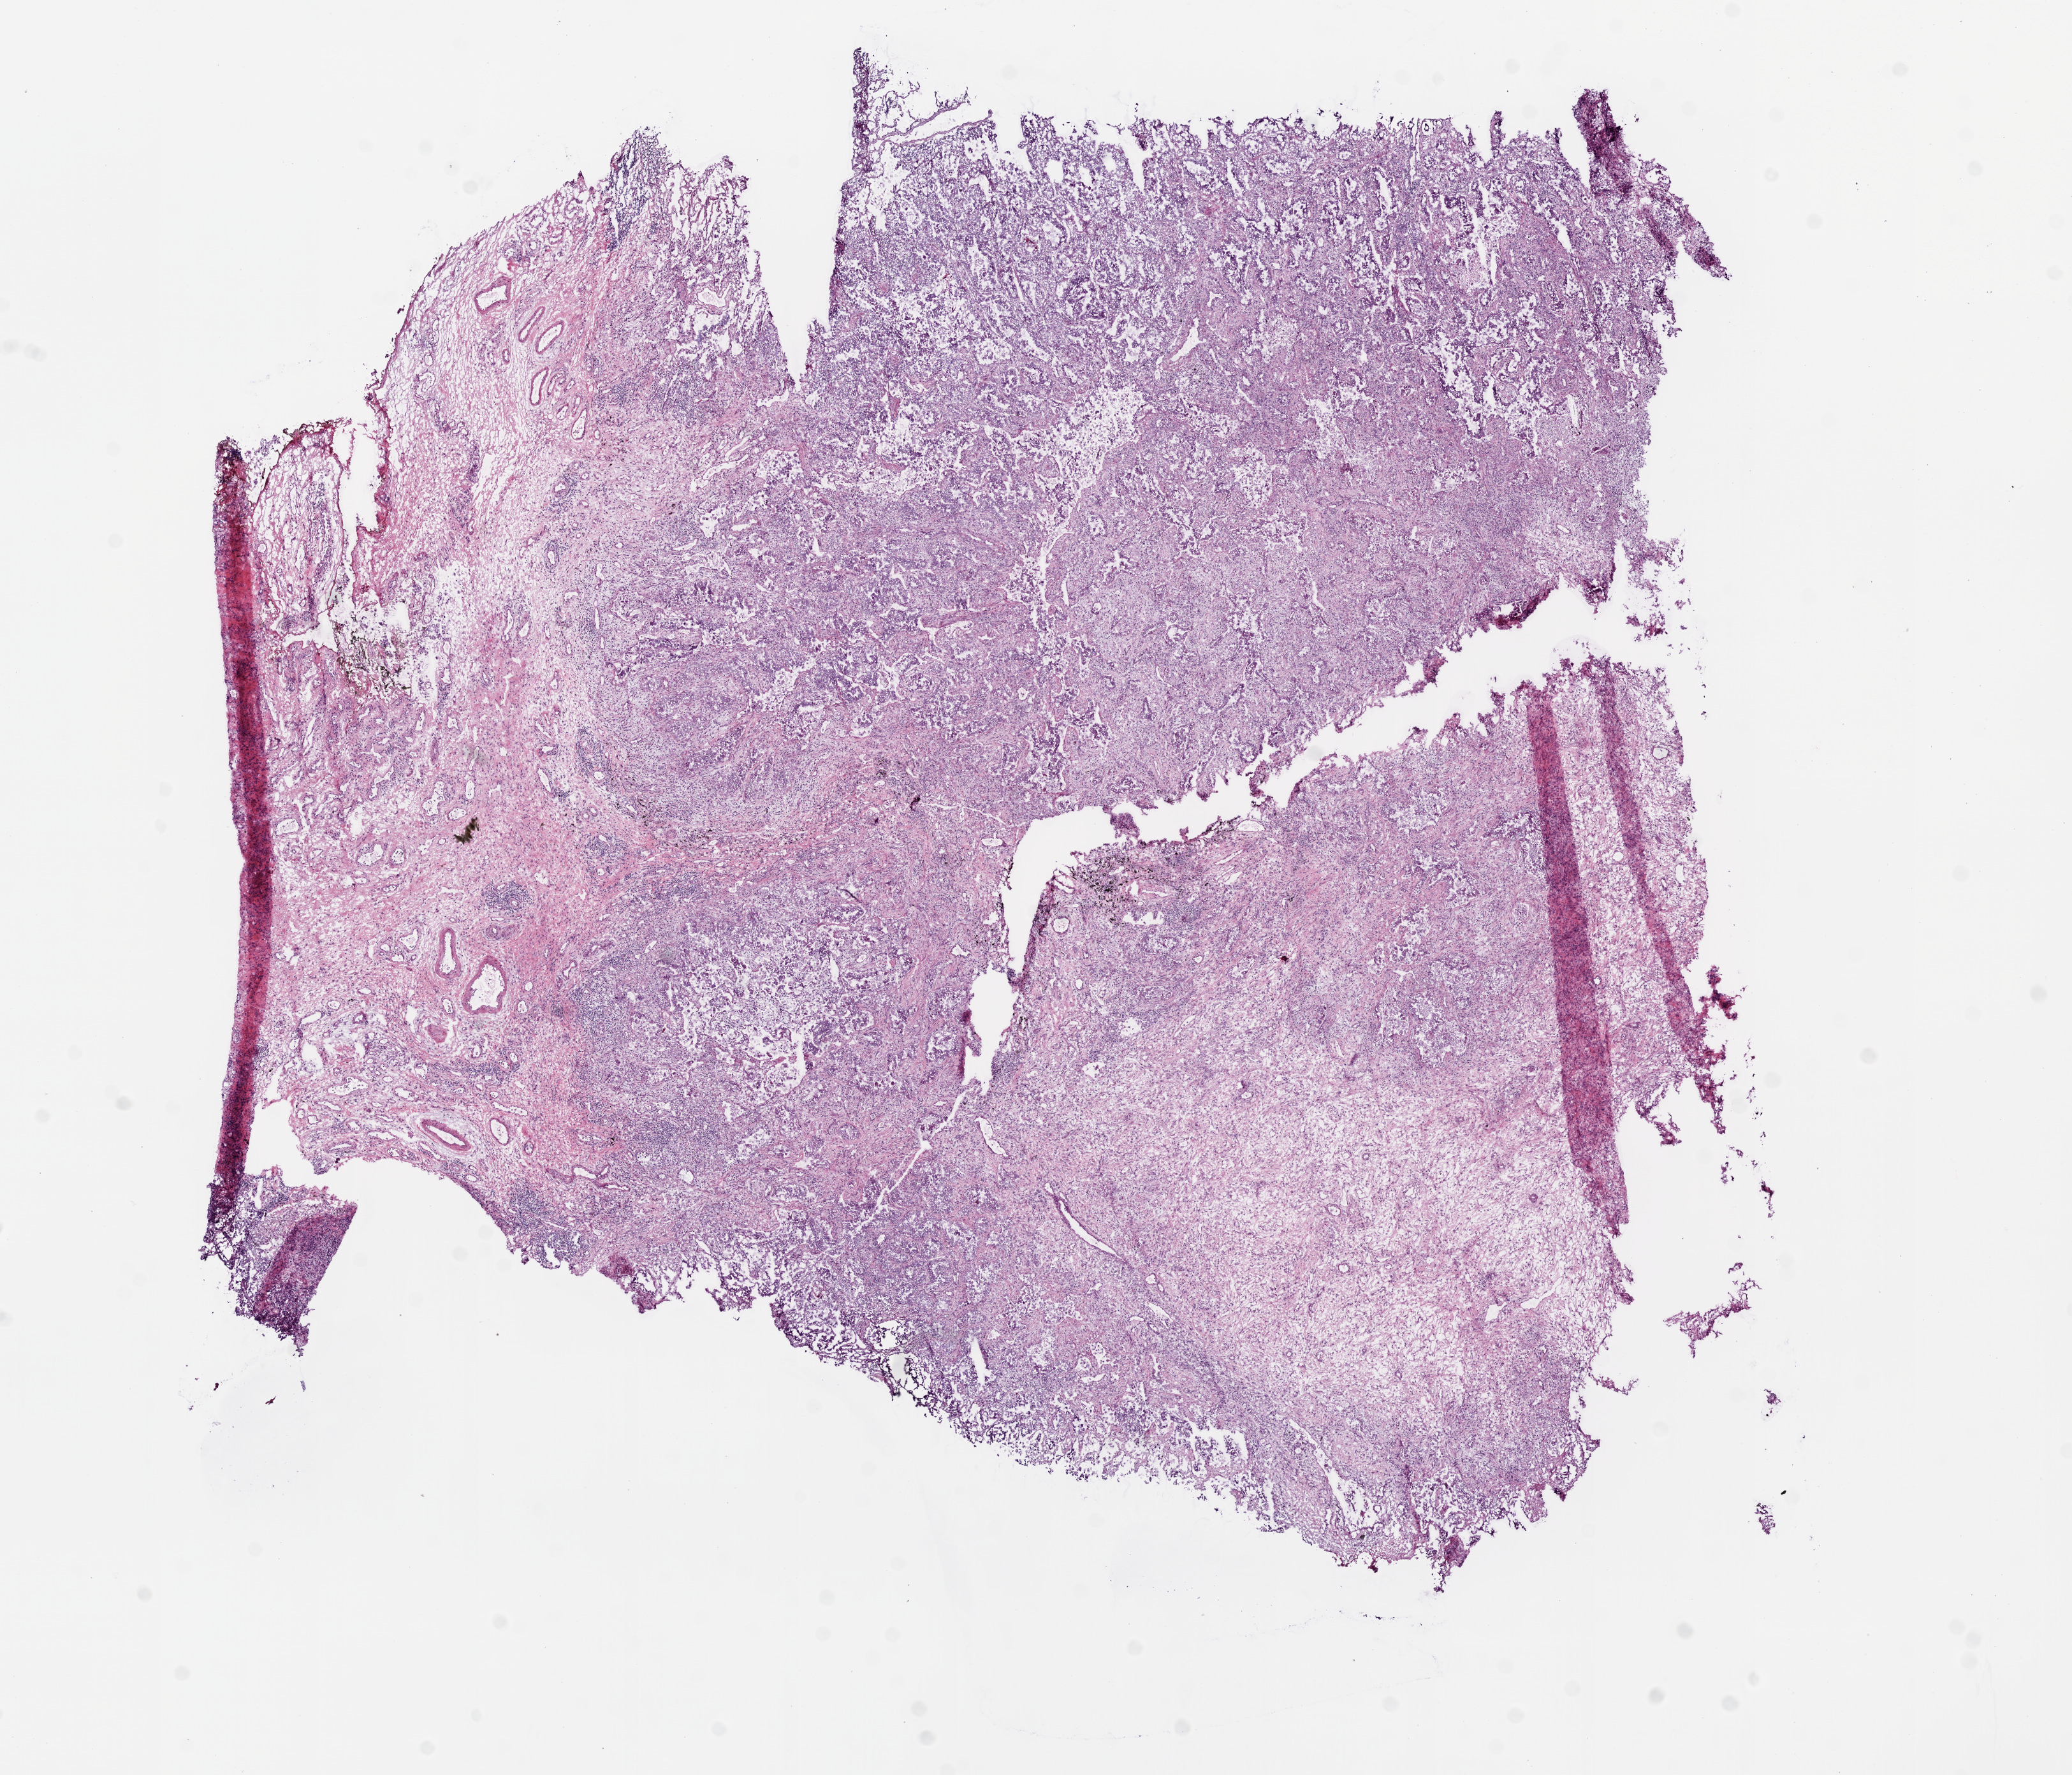
Whole-slide histology image, Hematoxylin and eosin (H&E) stained, low-resolution overview of the scanned area, about 13.0 x 11.2 mm (acquisition: 20x scan). Frozen section from the bottom of the tissue portion. Primary tumour sample from the lung. Female, age 80 years at initial diagnosis. Slide review estimates, as recorded: tumour cells 50%, tumour nuclei 60%, normal cells 0%, stromal cells 50%, necrosis 0%.
• AJCC pathologic stage: IB
• diagnosis: Adenocarcinoma, NOS (lower lobe, lung)